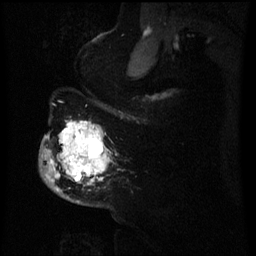
Breast MRI (dynamic contrast-enhanced), one sagittal slice. Position 47 of 60 along the scan axis. Dynamic contrast-enhanced series, image 2 of 3 at this slice position (ordered by acquisition). 1.5 T. TE 4.2 ms, TR 8 ms. 2.5 mm slice thickness. 256 × 256 image matrix, field of view 200 × 200 mm. Patient: female, 50 years.
Outlined on this slice (semi-automatically segmented with operator editing):
- analysis volume of interest (the breast-tissue region the enhancement analysis was run in; not a lesion): bounding box [x1, y1, x2, y2] px = [45, 122, 110, 185]
- tumour enhancement mask (voxels above the 70 % enhancement threshold inside the analysis volume of interest): [50, 126, 106, 177]